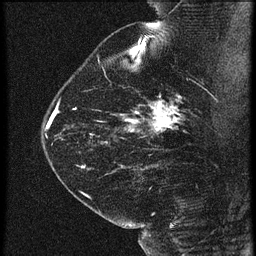
Breast MRI (dynamic contrast-enhanced), one sagittal slice; slice 43 of 60 in the series (ordered by position); 3 images stored at this slice position (order not interpretable as contrast timing); 1.5 T; TE 4.2 ms, TR 21.3 ms; 1.5 mm slice thickness; 256 × 256 image matrix. Patient: female, 42 years. From the clinical record (not read from this slice): setting: breast cancer imaged before/during neoadjuvant chemotherapy; receptor status: HER2-positive.
Annotated regions visible in this slice (semi-automatic segmentation, software-assisted and operator-edited):
- analysis volume of interest (the breast-tissue region the enhancement analysis was run in; not a lesion): bounding box (x1, y1, x2, y2) in pixels: (122, 82, 195, 147)
- tumour enhancement mask (voxels above the 90 % enhancement threshold inside the analysis volume of interest): (125, 100, 177, 133)